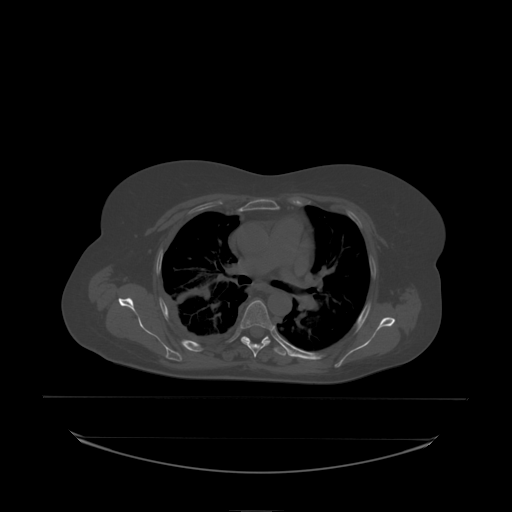
CT including the spine, one axial slice; position 156 of 242 along the scan axis; bone window (W 1800 / L 400 HU); 2.5 mm slice thickness; 512 × 512 image matrix, field of view 500 × 500 mm. Patient: female, 53 years. Case-level facts recorded for this patient, not image findings: primary cancer: lung.
Annotated regions visible in this slice (semi-automatically segmented with operator editing):
- T5 vertebra: bounding box [x1, y1, x2, y2] px = [241, 301, 272, 329]
- T6 vertebra: [241, 325, 273, 338]